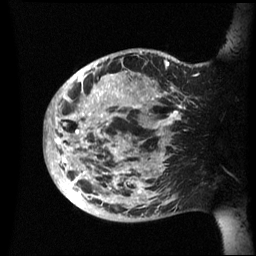
Breast MRI (dynamic contrast-enhanced), one sagittal slice. Slice 17 of 60 in the series (ordered by position). Dynamic contrast-enhanced series, image 2 of 3 at this slice position (ordered by acquisition). 1.5 T. TE 4.2 ms, TR 8.4 ms. 2.4 mm slice thickness. 256 × 256 image matrix. Female patient, age 48 years.
Outlined on this slice (semi-automatically segmented with operator editing):
- analysis volume of interest (the breast-tissue region the enhancement analysis was run in; not a lesion): bounding box <45,49,202,222> (left, top, right, bottom; pixels)
- tumour enhancement mask (voxels above the 70 % enhancement threshold inside the analysis volume of interest): <45,51,198,203>